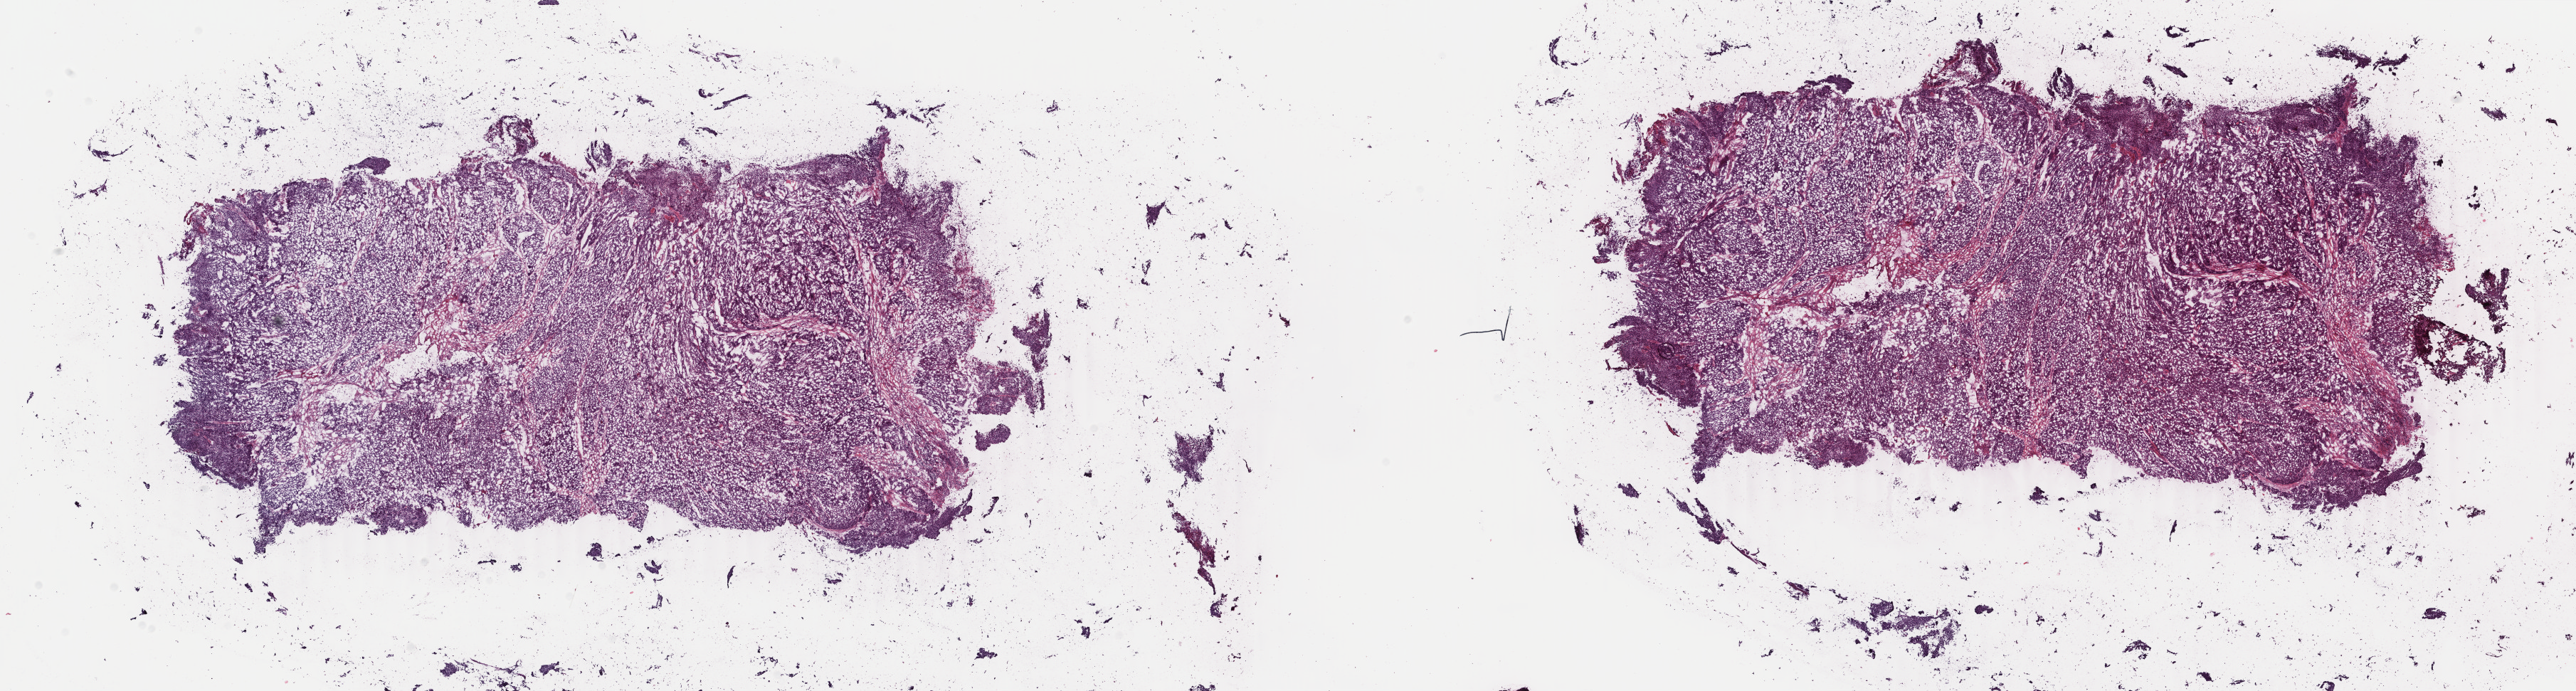
Digitized H&E-stained tissue section (whole slide) — shown as a low-resolution overview of the whole scanned area (about 28.8 x 7.7 mm). Frozen section. Primary tumour sample from the cervix. Female, age 48 years at initial diagnosis. Histologic grade: G3 (poorly differentiated). Composition of this section per pathologist review: tumour cells 79%, tumour nuclei 90%, normal cells 0%, stromal cells 20%, necrosis 1%. Inflammatory infiltration, as recorded: lymphocyte infiltration 2%, monocyte infiltration 0%, neutrophil infiltration 0%.
Histologic diagnosis: Squamous cell carcinoma, keratinizing, NOS (cervix uteri). FIGO stage: IB2.